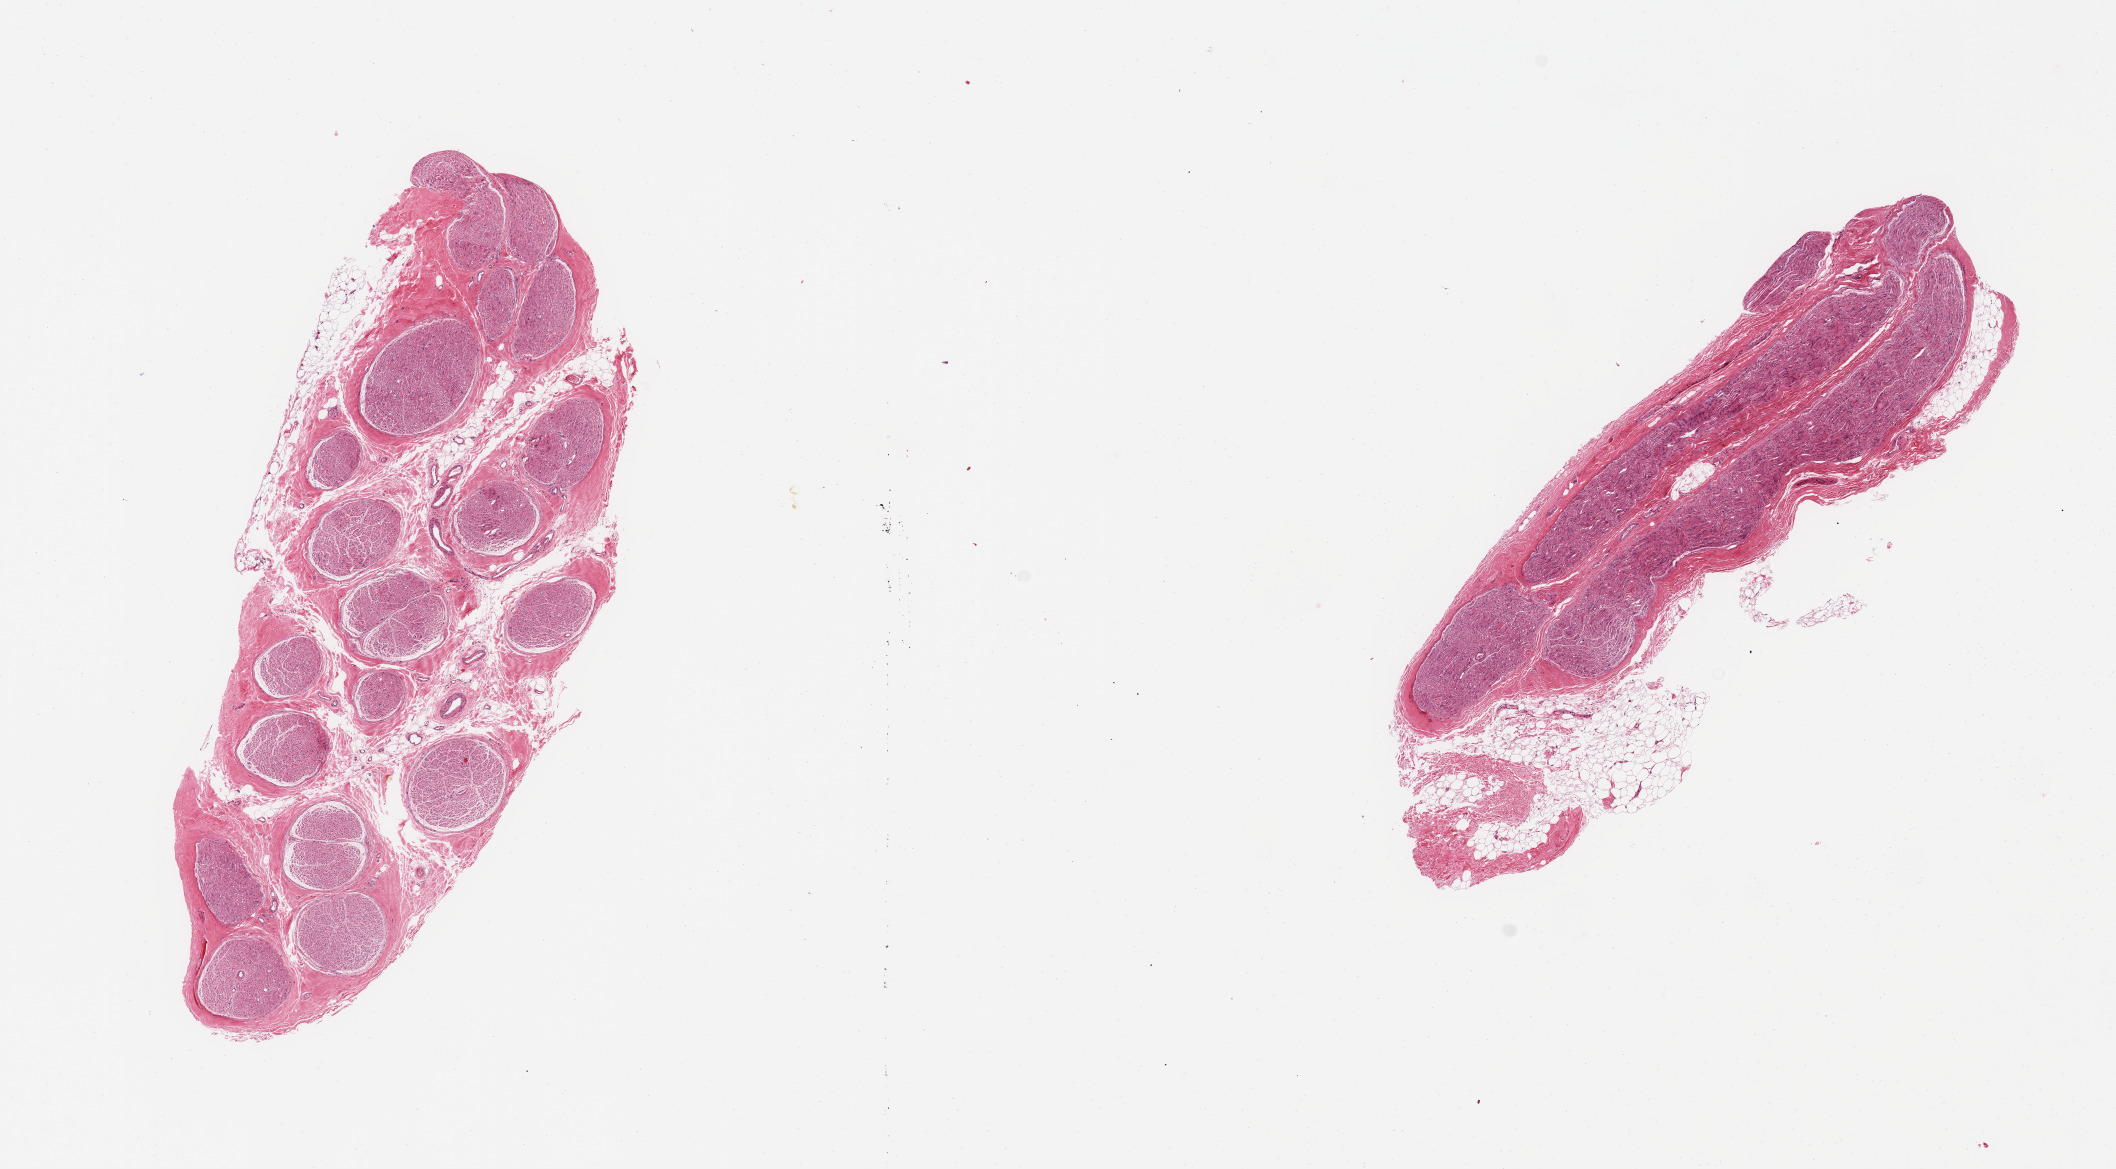
Whole-slide image, haematoxylin and eosin stain, low-resolution overview of the scanned area, about 16.7 x 9.2 mm. PAXgene-fixed paraffin-embedded (PFPE) section. Sampled site (target tissue): tibial nerve. Donor tissue sample. Male donor.
Review note (as recorded): 2 pieces; 10% fibrofatty content, internal and external.